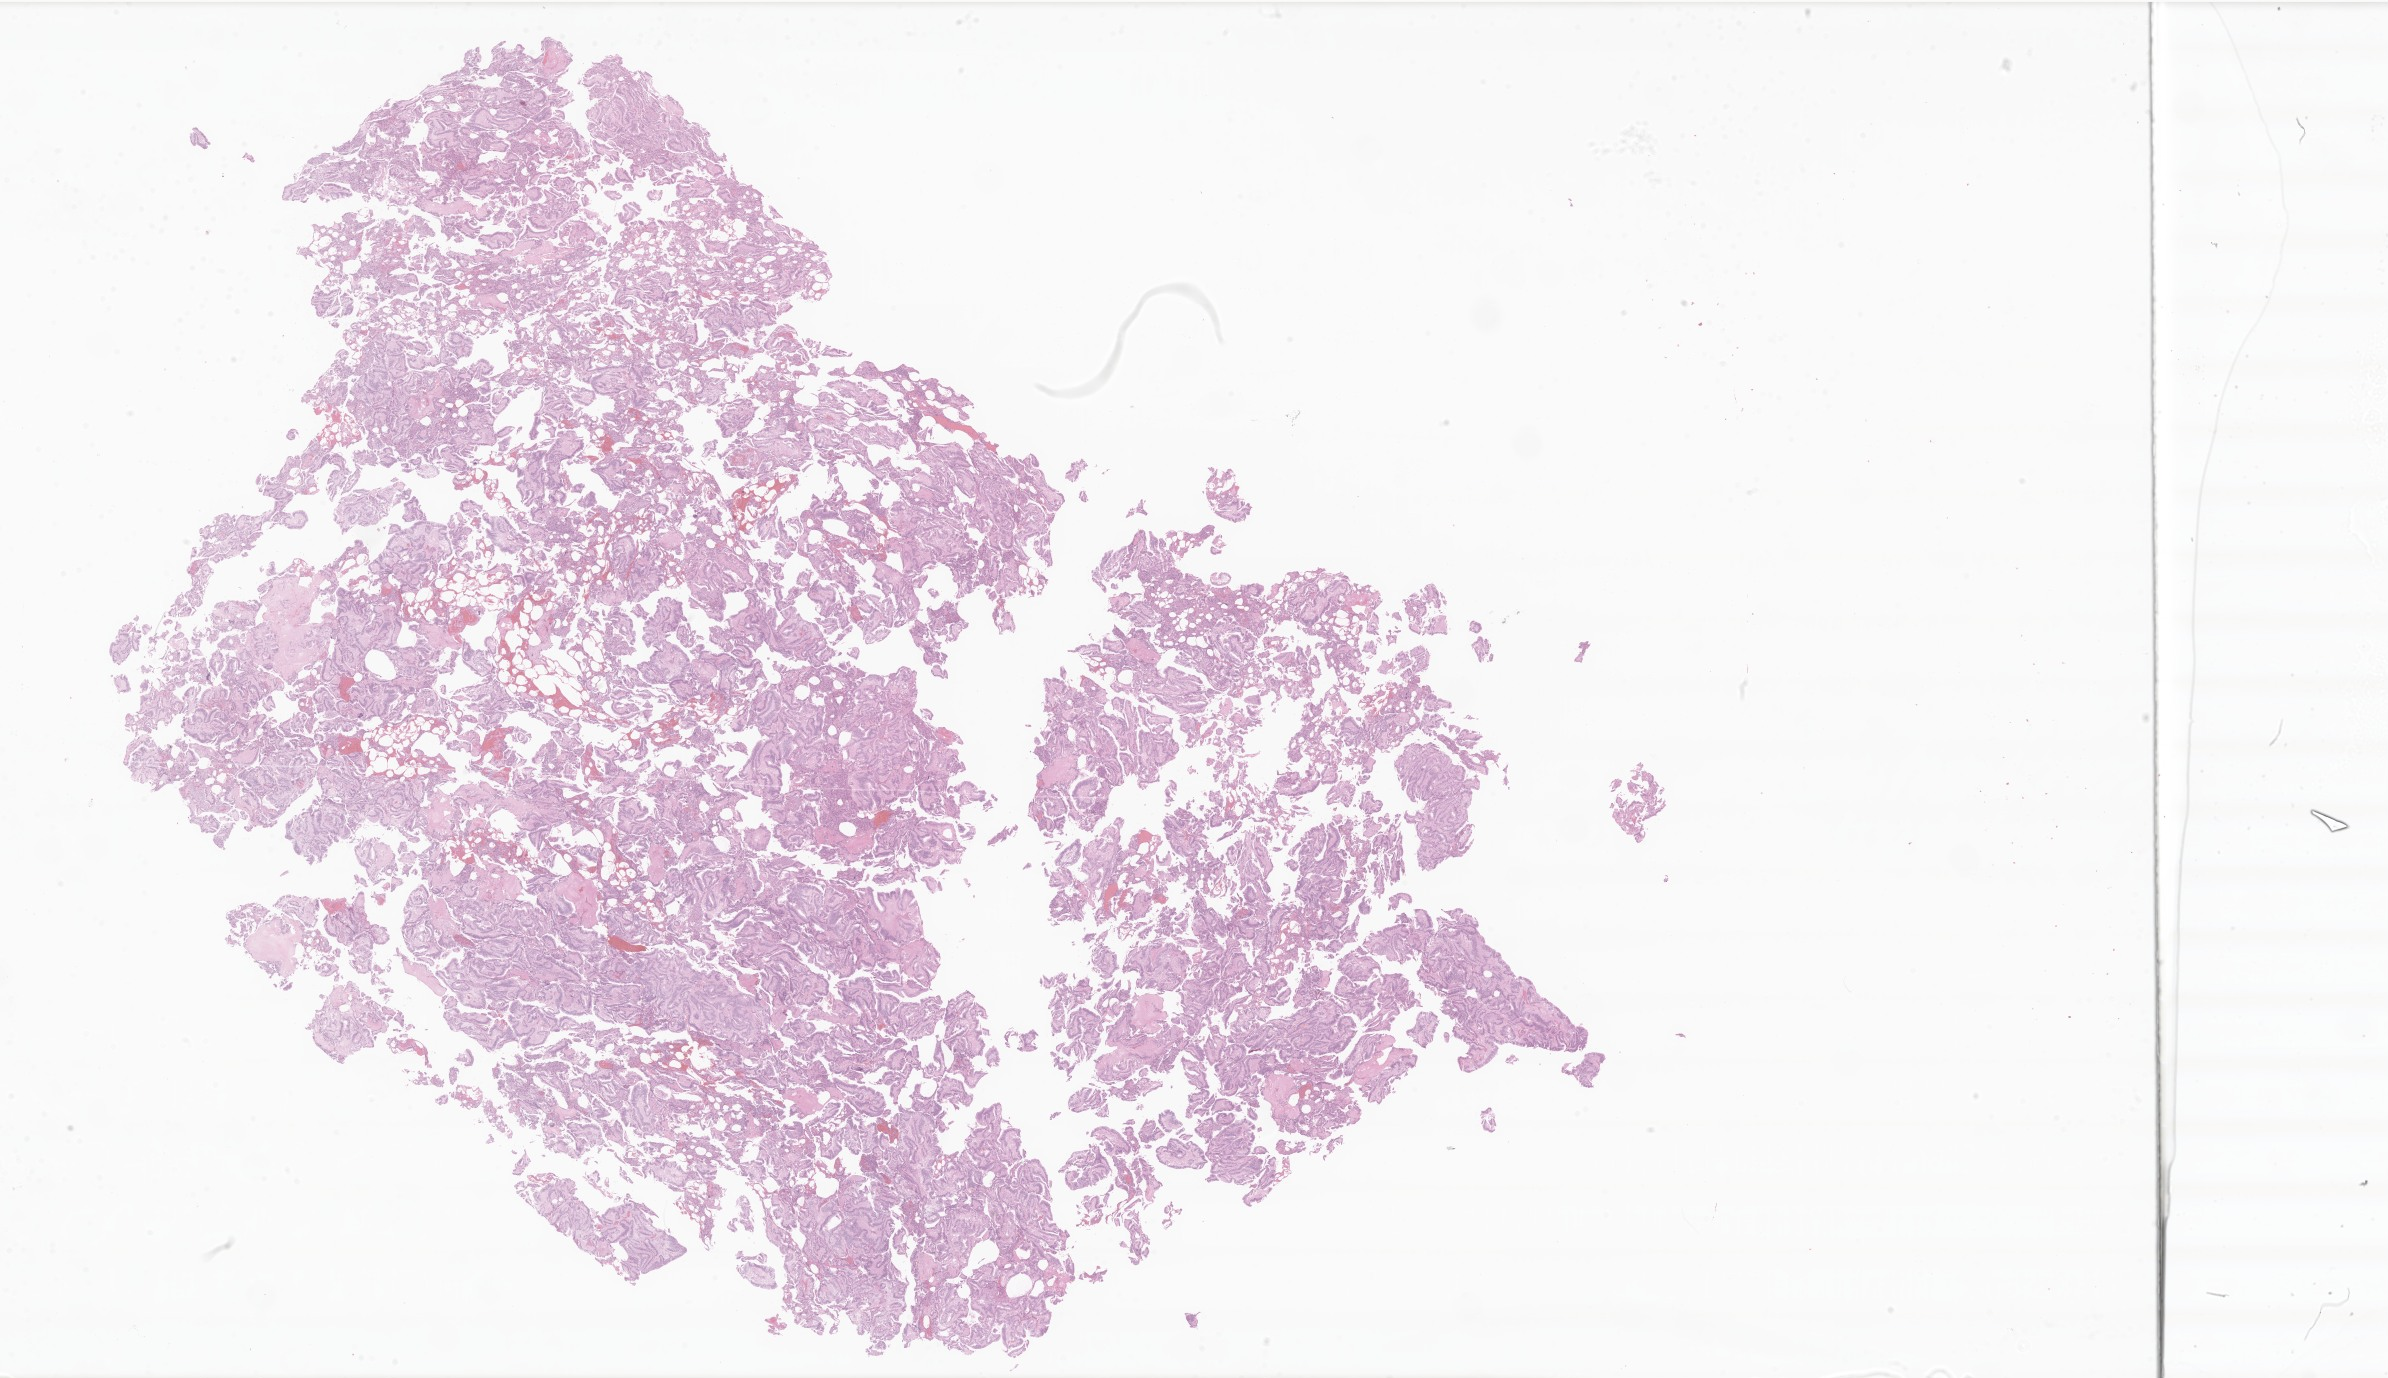
Whole-slide image, H&E stain of tumor tissue from the cerebral ventricle, shown as a low-resolution overview of the whole scanned area (about 40.3 x 23.2 mm). FFPE section. Male patient, age 126 months (10 years 6 months).
Recorded diagnosis: Ependymoma, NOS.